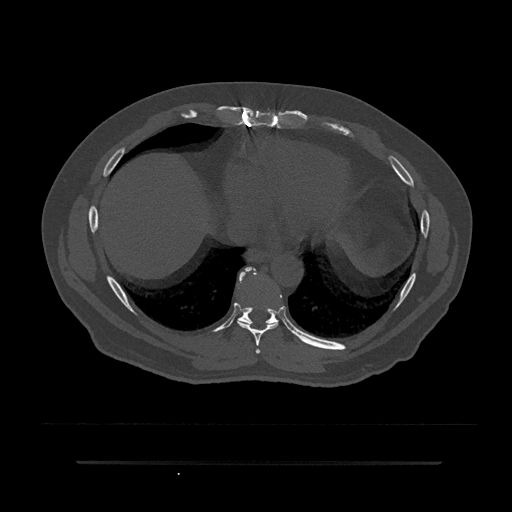
CT including the spine, one axial slice. Slice 406 of 797 in the series (ordered by position). 120 kVp. Bone window (W 1800 / L 400 HU). 0.5 mm slice thickness. 512 × 512 image matrix, field of view 464 × 464 mm. Male patient, age 59 years. Case-level facts recorded for this patient, not image findings: primary cancer: bile ducts.
Outlined on this slice (semi-automatic segmentation, software-assisted and operator-edited):
- T7 vertebra: bounding box (x1, y1, x2, y2) in pixels: (255, 349, 260, 354)
- T8 vertebra: (237, 267, 278, 346)
- T9 vertebra: (238, 267, 280, 325)